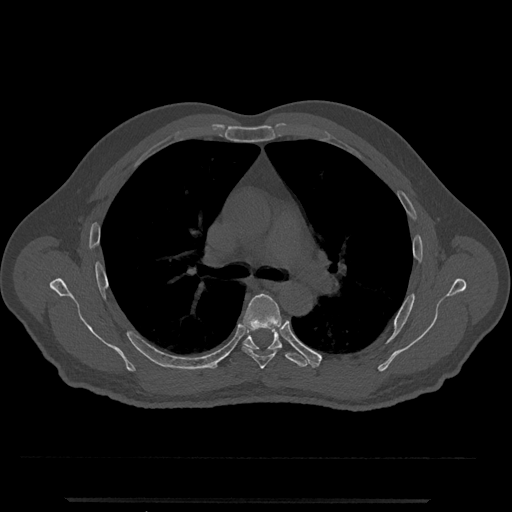
CT including the spine, one axial slice. Slice 769 of 797 in the series (ordered by position). Reconstruction kernel Br40s/3. 120 kVp. Bone window (W 1800 / L 400 HU). 512 × 512 image matrix, field of view 419 × 419 mm. Male patient, age 63 years. Case-level facts recorded for this patient, not image findings: primary cancer: prostate.
Annotated regions visible in this slice (semi-automatic segmentation, software-assisted and operator-edited):
- T5 vertebra: bounding box <243,293,281,369> (left, top, right, bottom; pixels)
- T6 vertebra: <230,330,307,367>